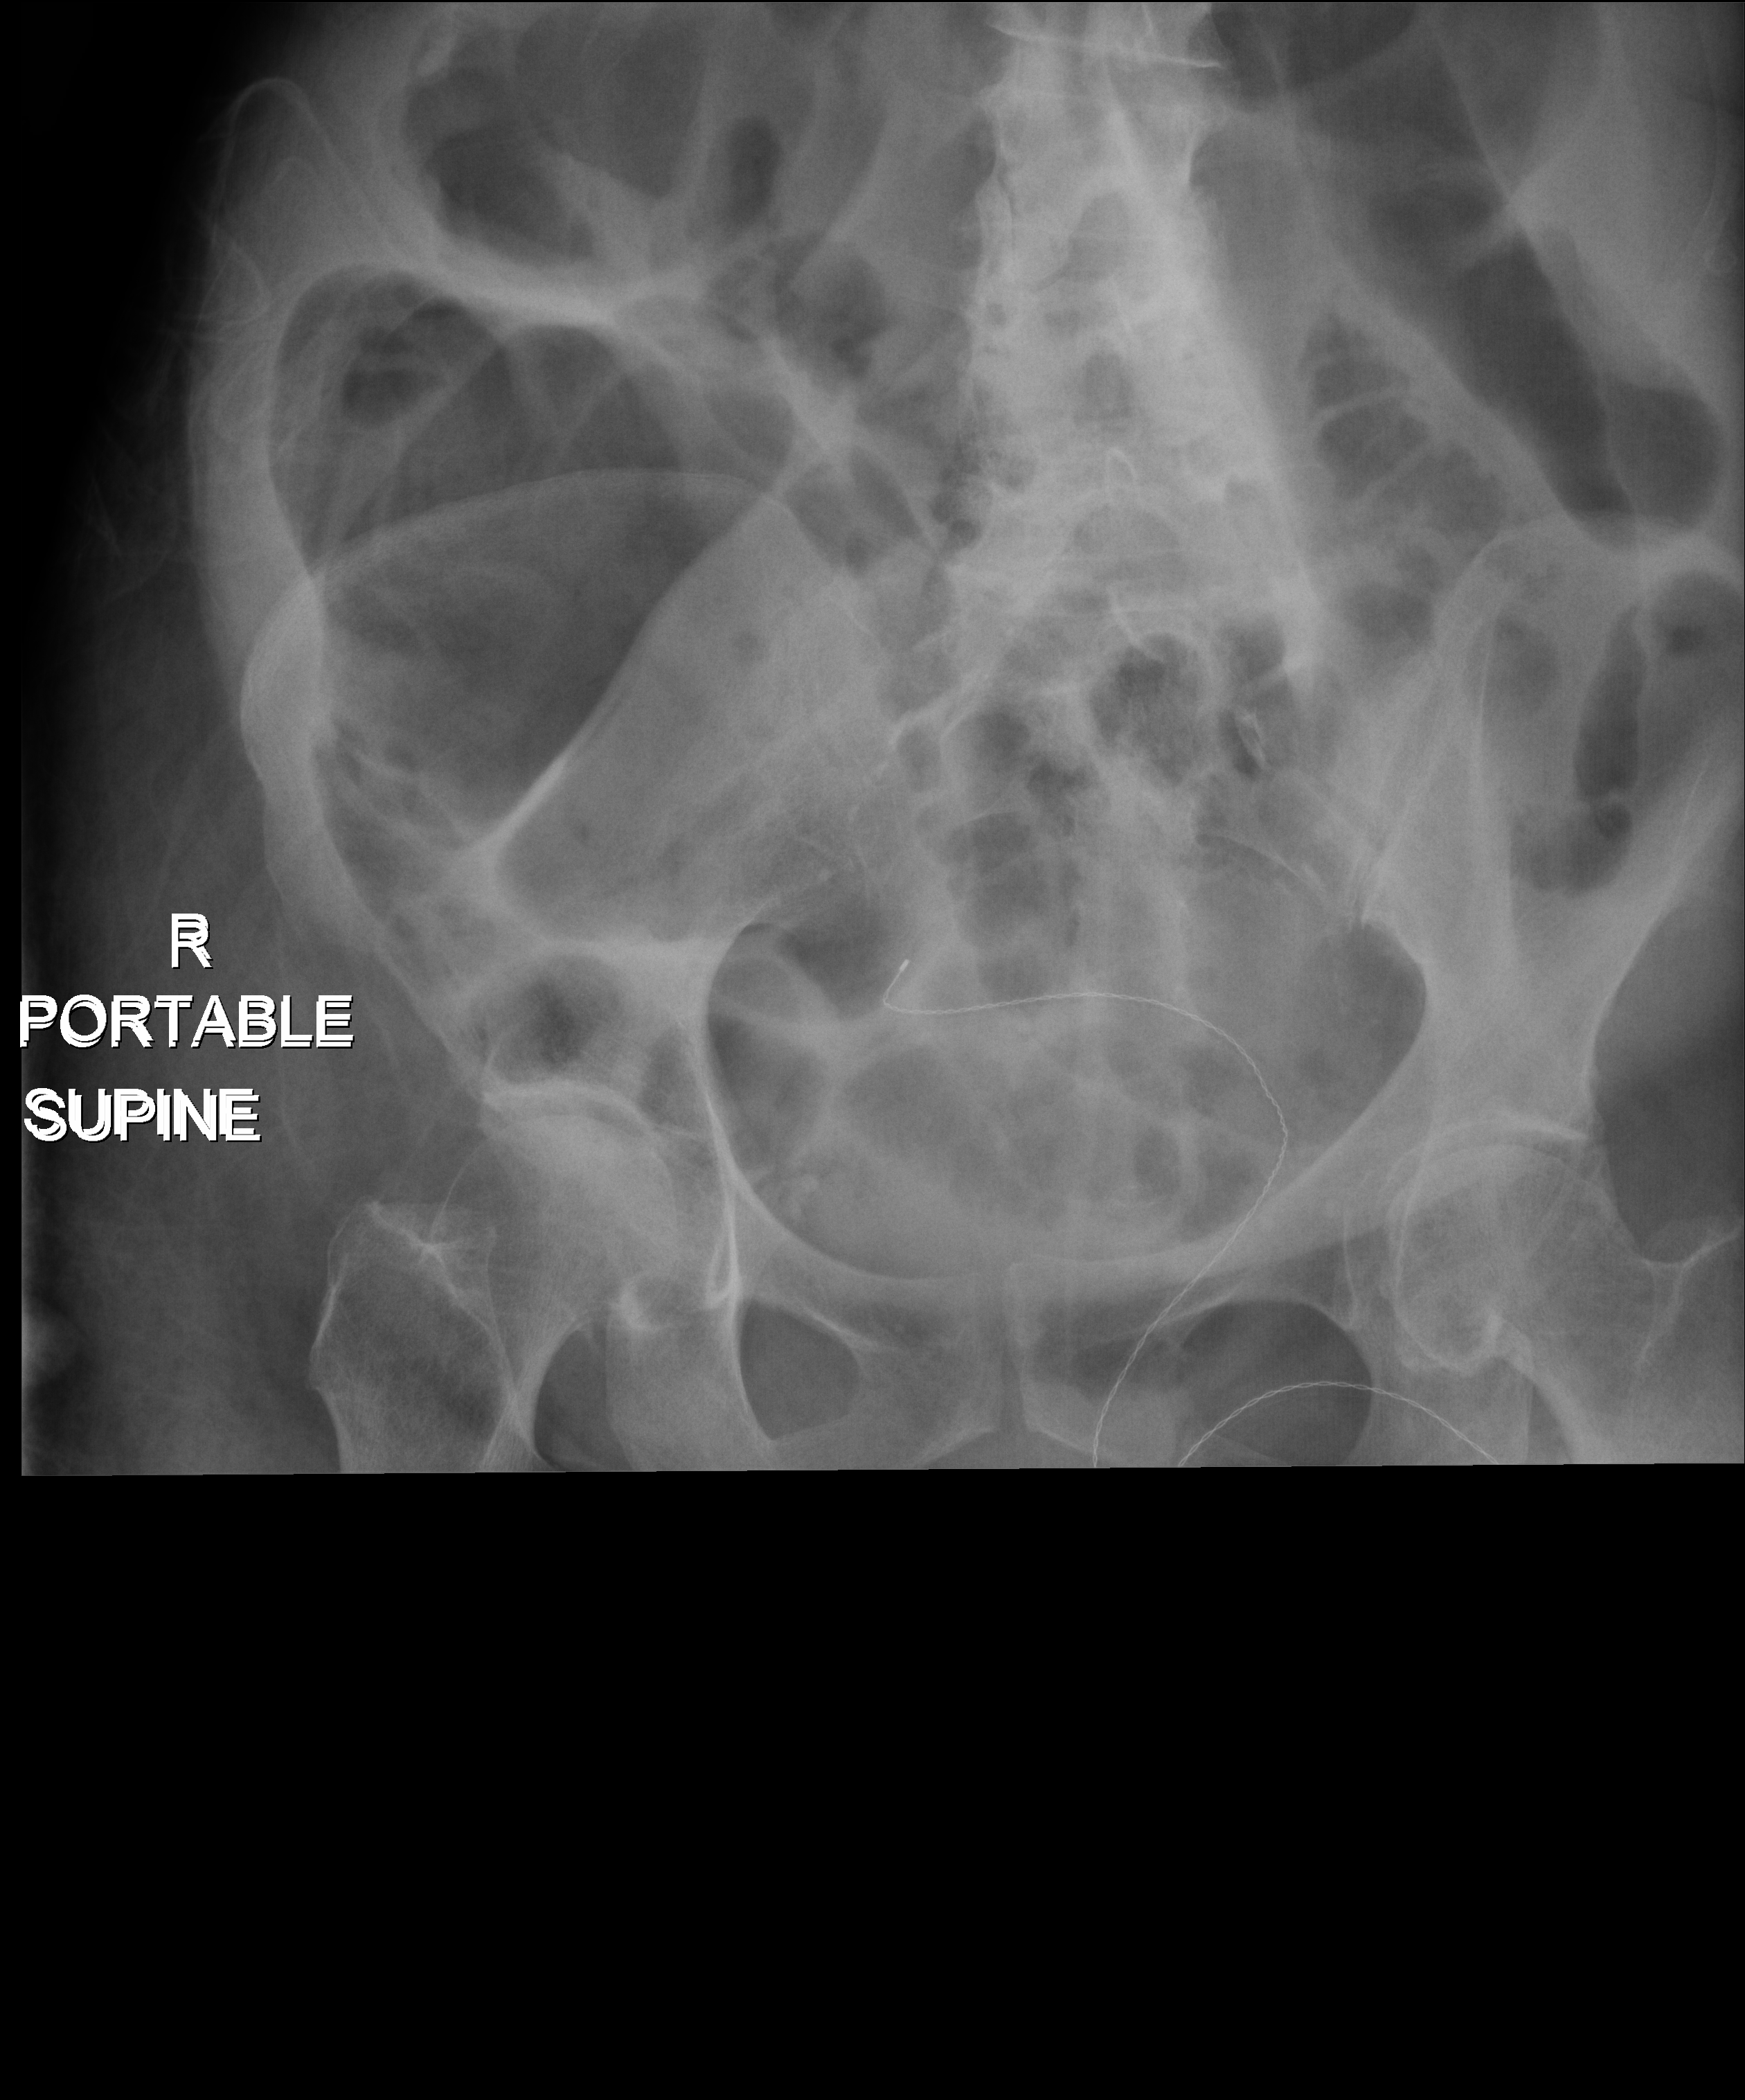
Abdomen X-ray (portable), anteroposterior (AP) projection. Patient hospitalised with COVID-19; female, aged 60–74 years.
From the hospital-stay record, not from the radiograph (when in the stay this image was taken is not recorded):
- admitted to intensive care during this hospital stay: yes